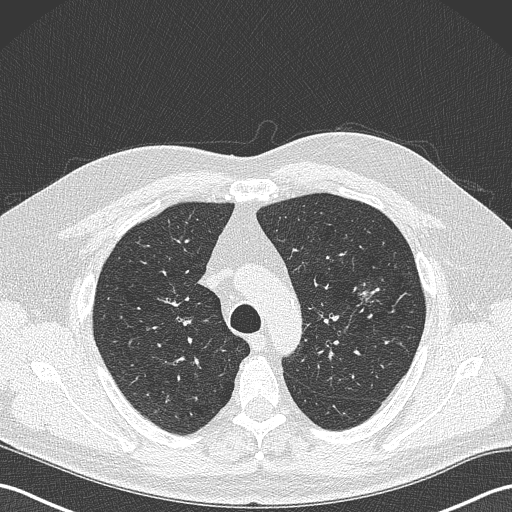
Low-dose screening chest CT, one axial slice; slice 255 of 343 in the series (ordered by position); reconstruction kernel B50f; 120 kVp; lung window (W 1500 / L -600 HU); 1 mm slice thickness; 512 × 512 image matrix, field of view 350 × 350 mm.
Outlined on this slice (expert manual segmentation):
- lesion 1 (tumor, upper lobe of left lung): bounding box [x1, y1, x2, y2] px = [358, 291, 372, 303]